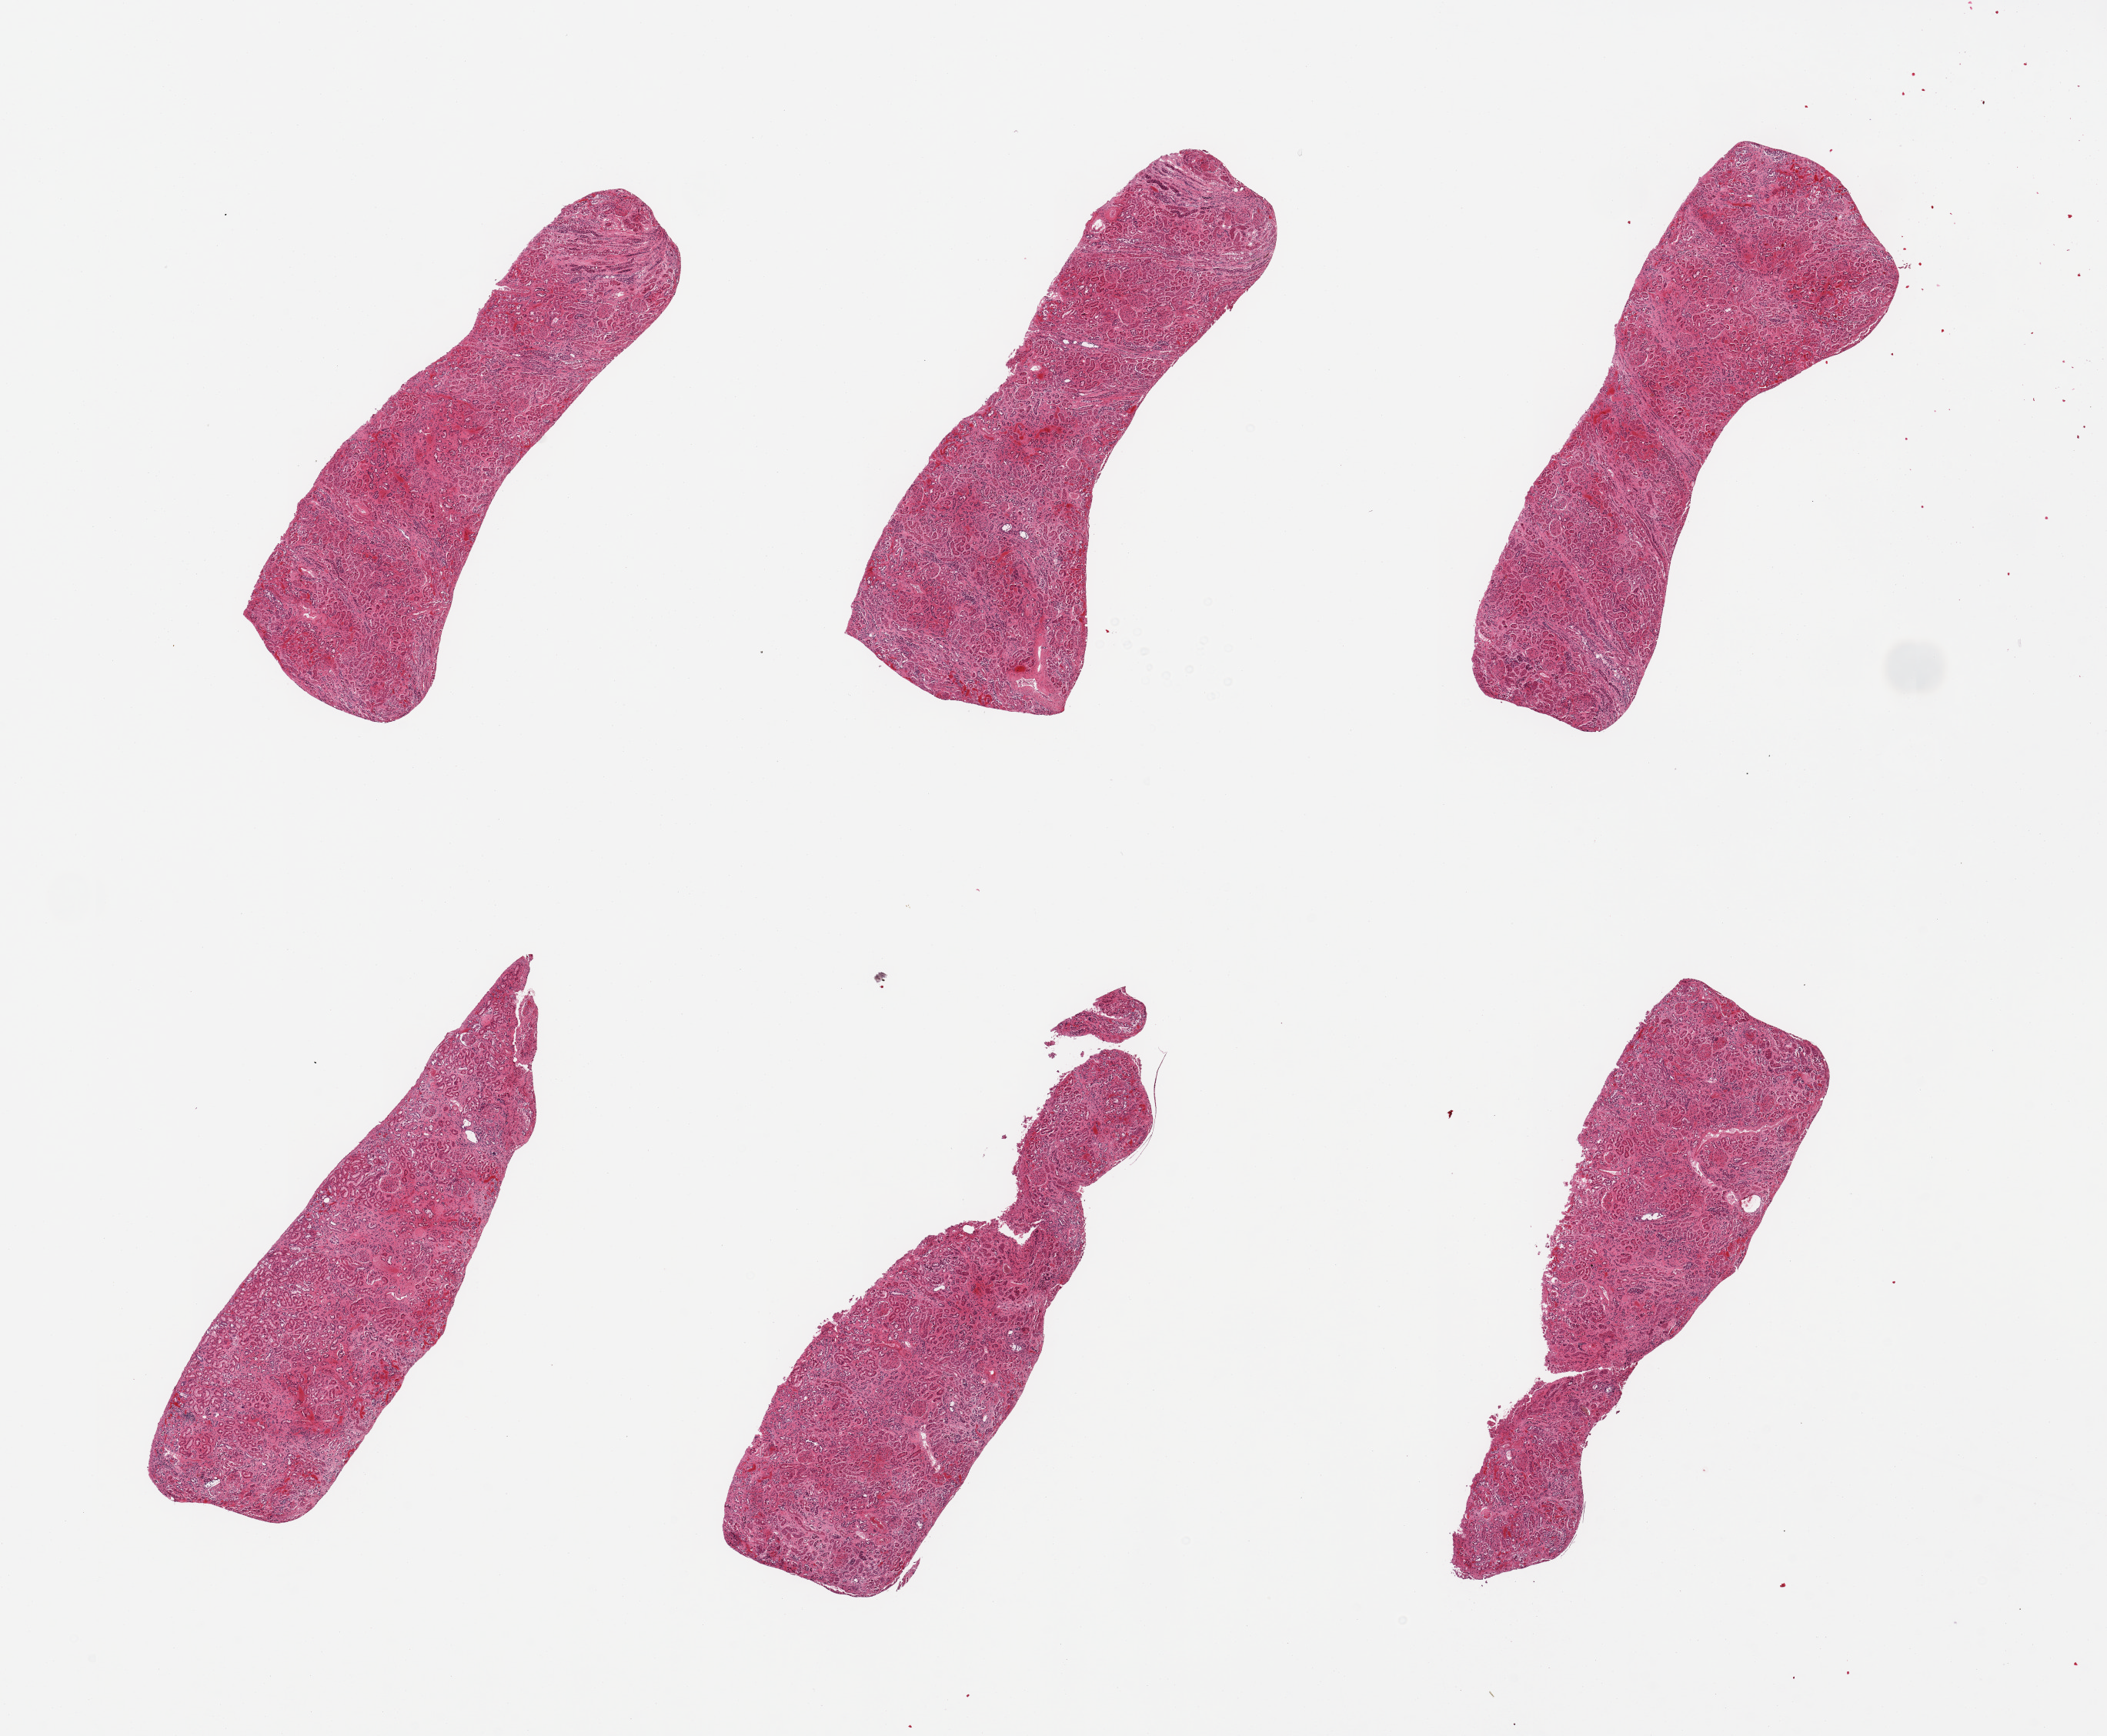
Digitized hematoxylin and eosin (H&E)-stained section, brightfield, low-resolution overview of the scanned area, about 21.7 x 17.8 mm (slide scanned at 20x); PAXgene-fixed paraffin-embedded (PFPE) section; section of renal cortex (target tissue); tissue donor sample. Male donor.
Review note (as recorded): 6 pieces; no lesions; tubules severely autolyzed.